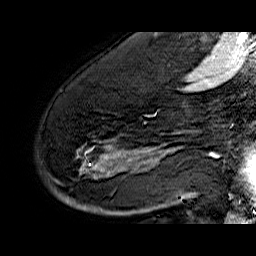
Breast MRI (dynamic contrast-enhanced), one sagittal slice; slice 42 of 60 in the series (ordered by position); dynamic contrast-enhanced series, time point 2 of 6 at this slice position (early post-contrast); 1.5 T; TE 6.4 ms, TR 32.9 ms; 256 × 256 image matrix, field of view 200 × 200 mm. Female patient. Case-level facts recorded for this patient, not image findings: setting: breast cancer imaged before/during neoadjuvant chemotherapy; receptor status: HR-positive, HER2-negative.
Outlined on this slice (semi-automatic segmentation, software-assisted and operator-edited):
- analysis volume of interest (the breast-tissue region the enhancement analysis was run in; not a lesion): bounding box (x1, y1, x2, y2) in pixels: (55, 74, 176, 210)
- tumour enhancement mask (voxels above the 100 % enhancement threshold inside the analysis volume of interest): (67, 145, 175, 203)